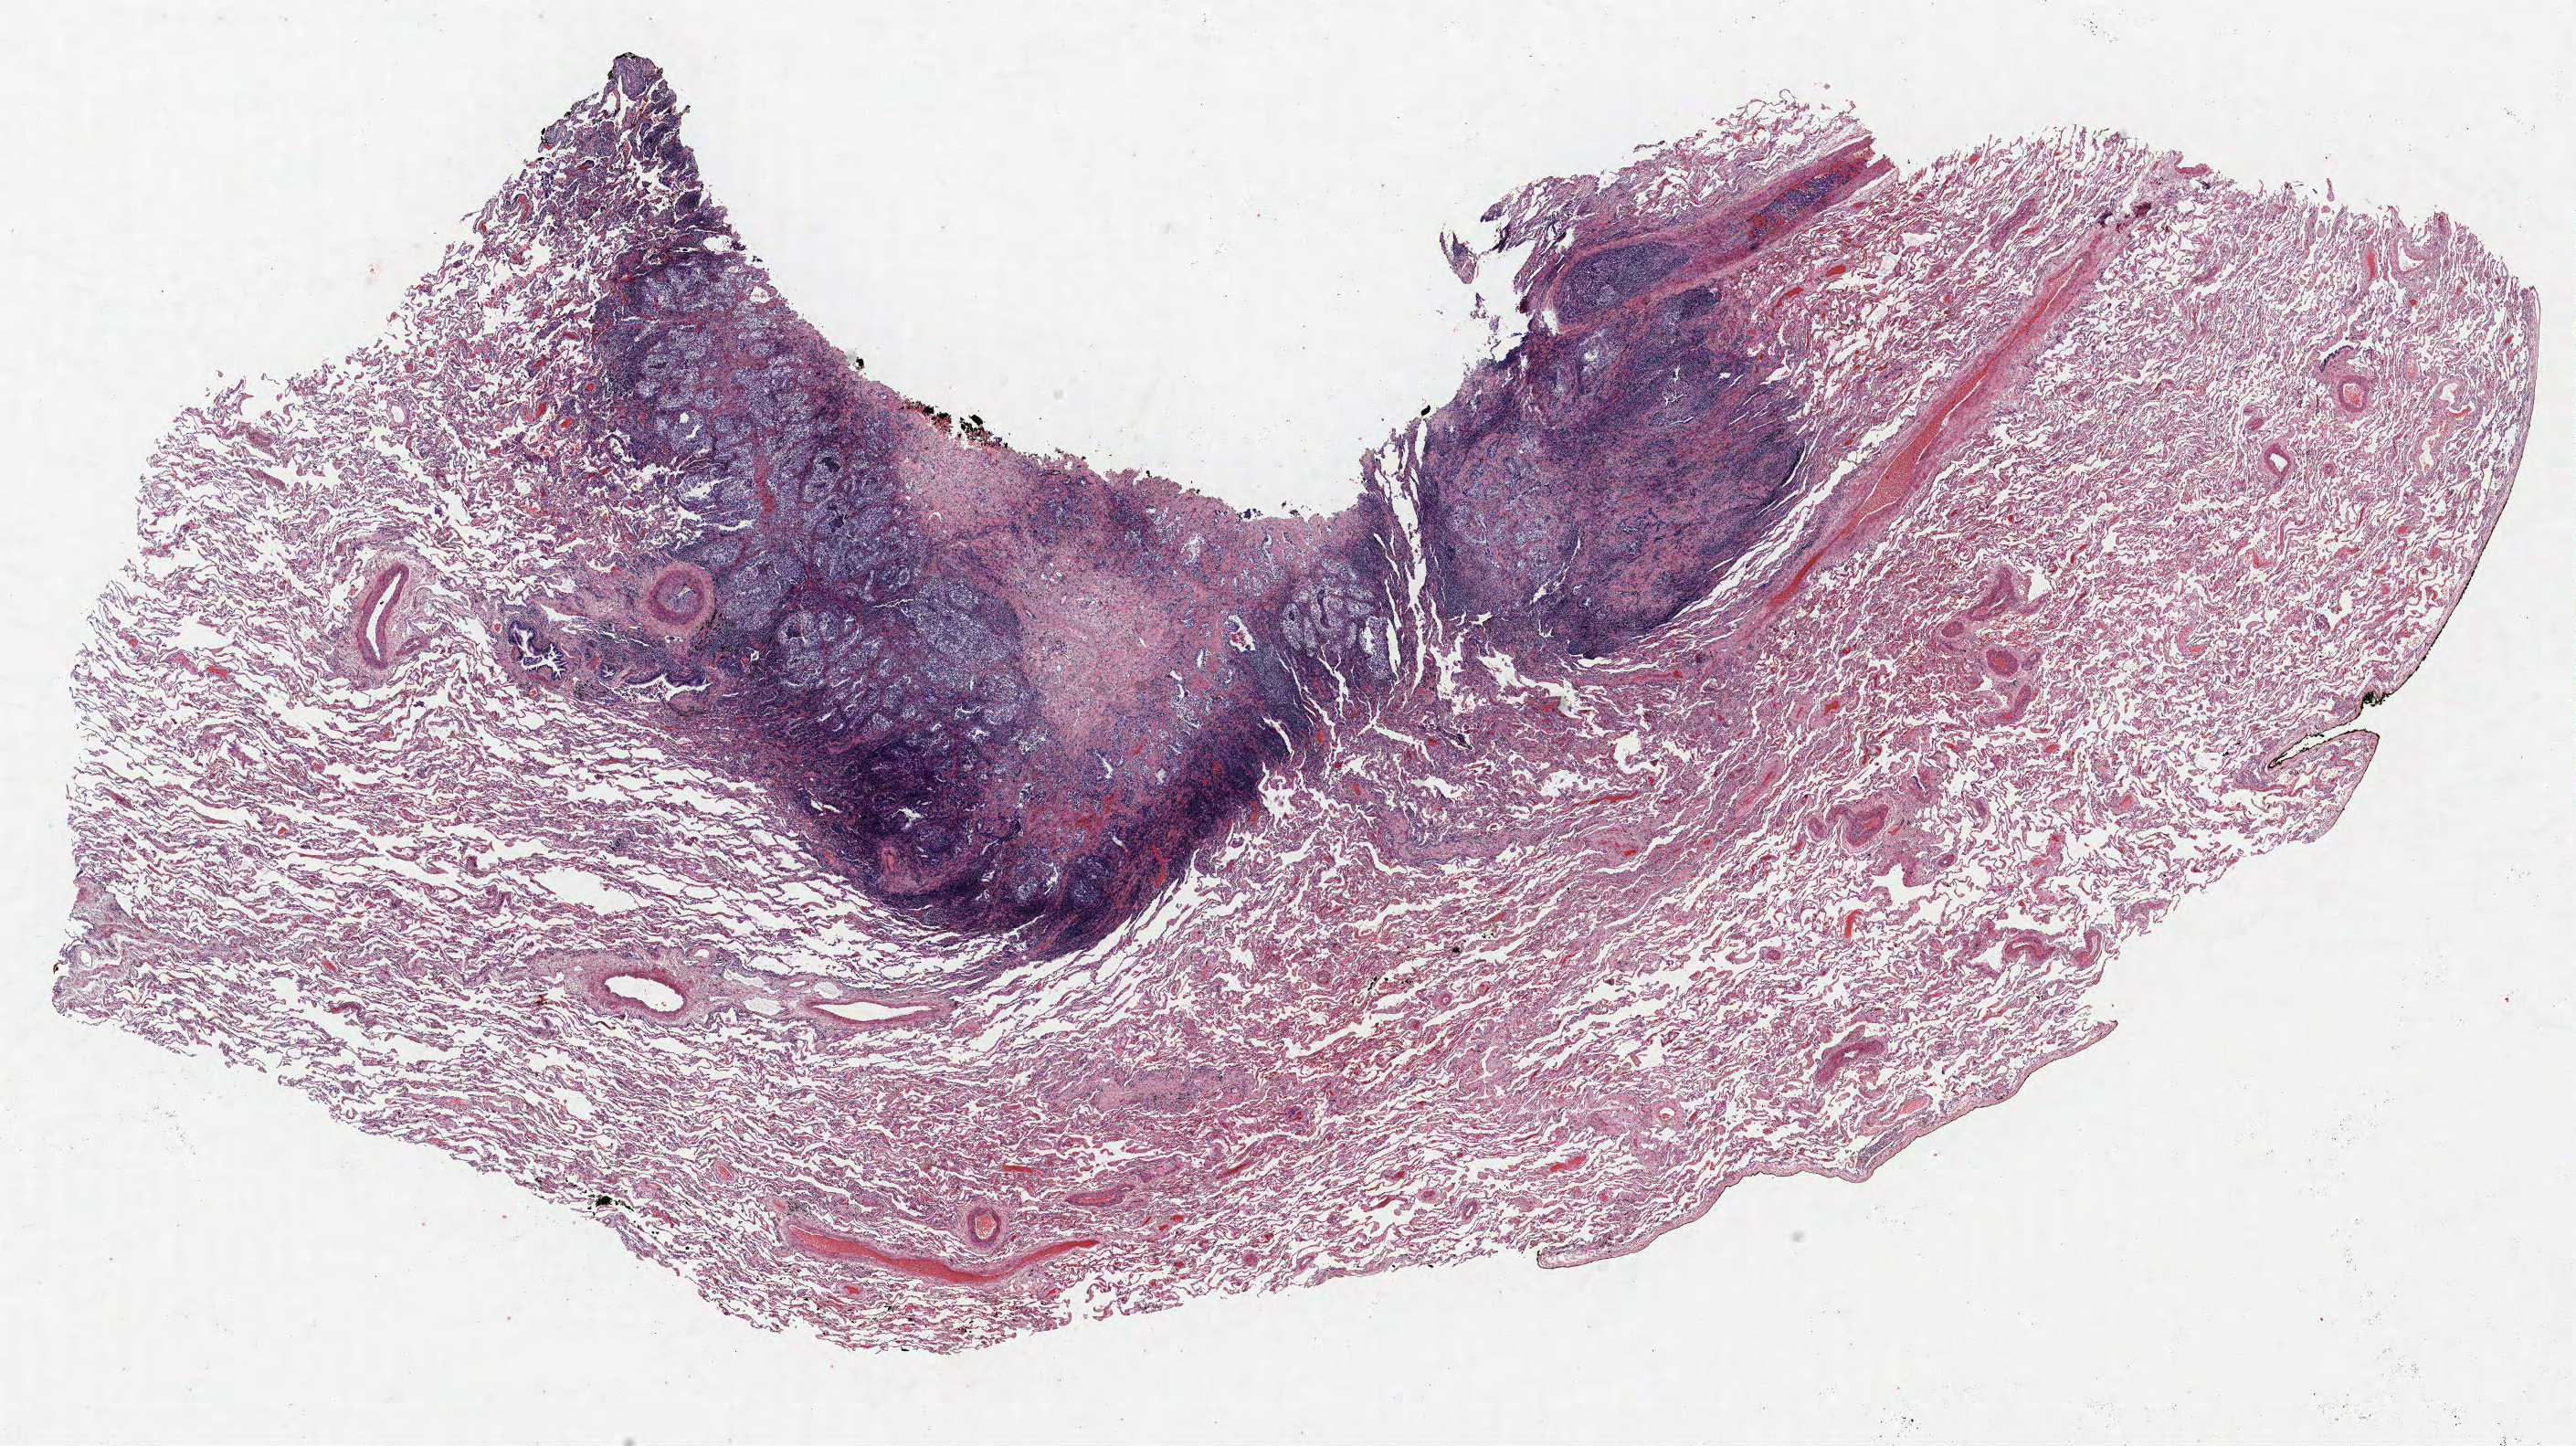
H&E-stained whole-slide image, a low-resolution overview of the entire scanned area, about 22.6 x 12.7 mm; FFPE section; lung. Female, age 60 at enrolment. Former smoker at enrolment. Grade: poorly differentiated (G3).
Stage (AJCC 6th edition): IB. Participant's lung-cancer diagnosis: Non-small cell carcinoma. Primary tumour location (clinical record): left upper lobe. Tumour size (pathology): 16 mm.